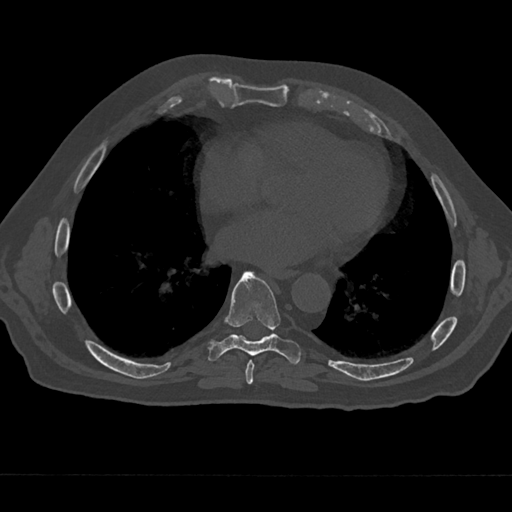
CT including the spine, one axial slice; position 319 of 797 along the scan axis; reconstruction kernel Br40s/3; 120 kVp; bone window (W 1800 / L 400 HU); 0.5 mm slice thickness; 512 × 512 image matrix, field of view 377 × 377 mm. Male patient, age 75 years. Case-level facts recorded for this patient, not image findings: primary cancer: renal.
Structures marked on this image (semi-automatically segmented with operator editing):
- T7 vertebra: box from (x=243, y=359) to (x=255, y=385) px
- T8 vertebra: (x=207, y=271)–(x=301, y=365)